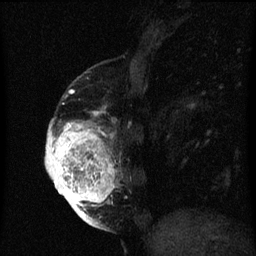
Breast MRI (dynamic contrast-enhanced), one sagittal slice. Slice 19 of 60 in the series (ordered by position). Dynamic contrast-enhanced series, image 2 of 3 at this slice position (ordered by acquisition). 1.5 T. TE 4.2 ms, TR 8 ms. 2 mm slice thickness. 256 × 256 image matrix, field of view 180 × 180 mm. Patient: female, 56 years.
Outlined on this slice (semi-automatic segmentation, software-assisted and operator-edited):
- analysis volume of interest (the breast-tissue region the enhancement analysis was run in; not a lesion): bounding box <46,112,121,219> (left, top, right, bottom; pixels)
- tumour enhancement mask (voxels above the 70 % enhancement threshold inside the analysis volume of interest): <46,112,115,219>